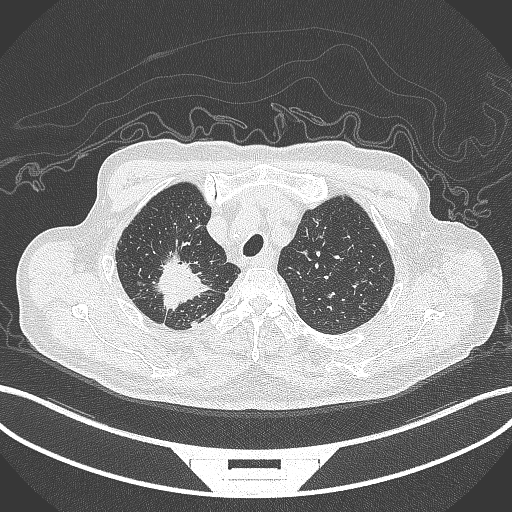
Chest CT, one axial slice; slice 320 of 407 in the series (ordered by position); lung window (W 1500 / L -600 HU); 512 × 512 image matrix, field of view 400 × 400 mm. Male patient, age 69 years. From the clinical record (not read from this slice): clinical TNM (as recorded): T1c N1 M1.
Structures marked on this image (bounding box drawn by a radiologist):
- lung tumour (recorded histology: adenocarcinoma): bounding box (x1, y1, x2, y2) in pixels: (140, 243, 214, 312)